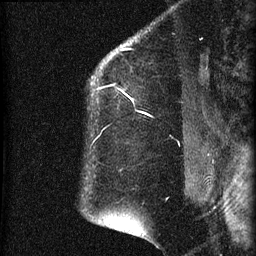
Breast MRI (dynamic contrast-enhanced), one sagittal slice; position 53 of 60 along the scan axis; dynamic contrast-enhanced series, image 2 of 4 at this slice position (ordered by acquisition); 1.5 T; TE 4.2 ms, TR 22.7 ms; 1.5 mm slice thickness; 256 × 256 image matrix, field of view 180 × 180 mm. Patient: female, 35 years. From the clinical record (not read from this slice): setting: breast cancer imaged before/during neoadjuvant chemotherapy; receptor status: HR-positive, HER2-negative.
Structures marked on this image (semi-automatically segmented with operator editing):
- analysis volume of interest (the breast-tissue region the enhancement analysis was run in; not a lesion): bounding box (x1, y1, x2, y2) in pixels: (84, 27, 199, 112)
- tumour enhancement mask (voxels above the 90 % enhancement threshold inside the analysis volume of interest): (92, 83, 141, 112)